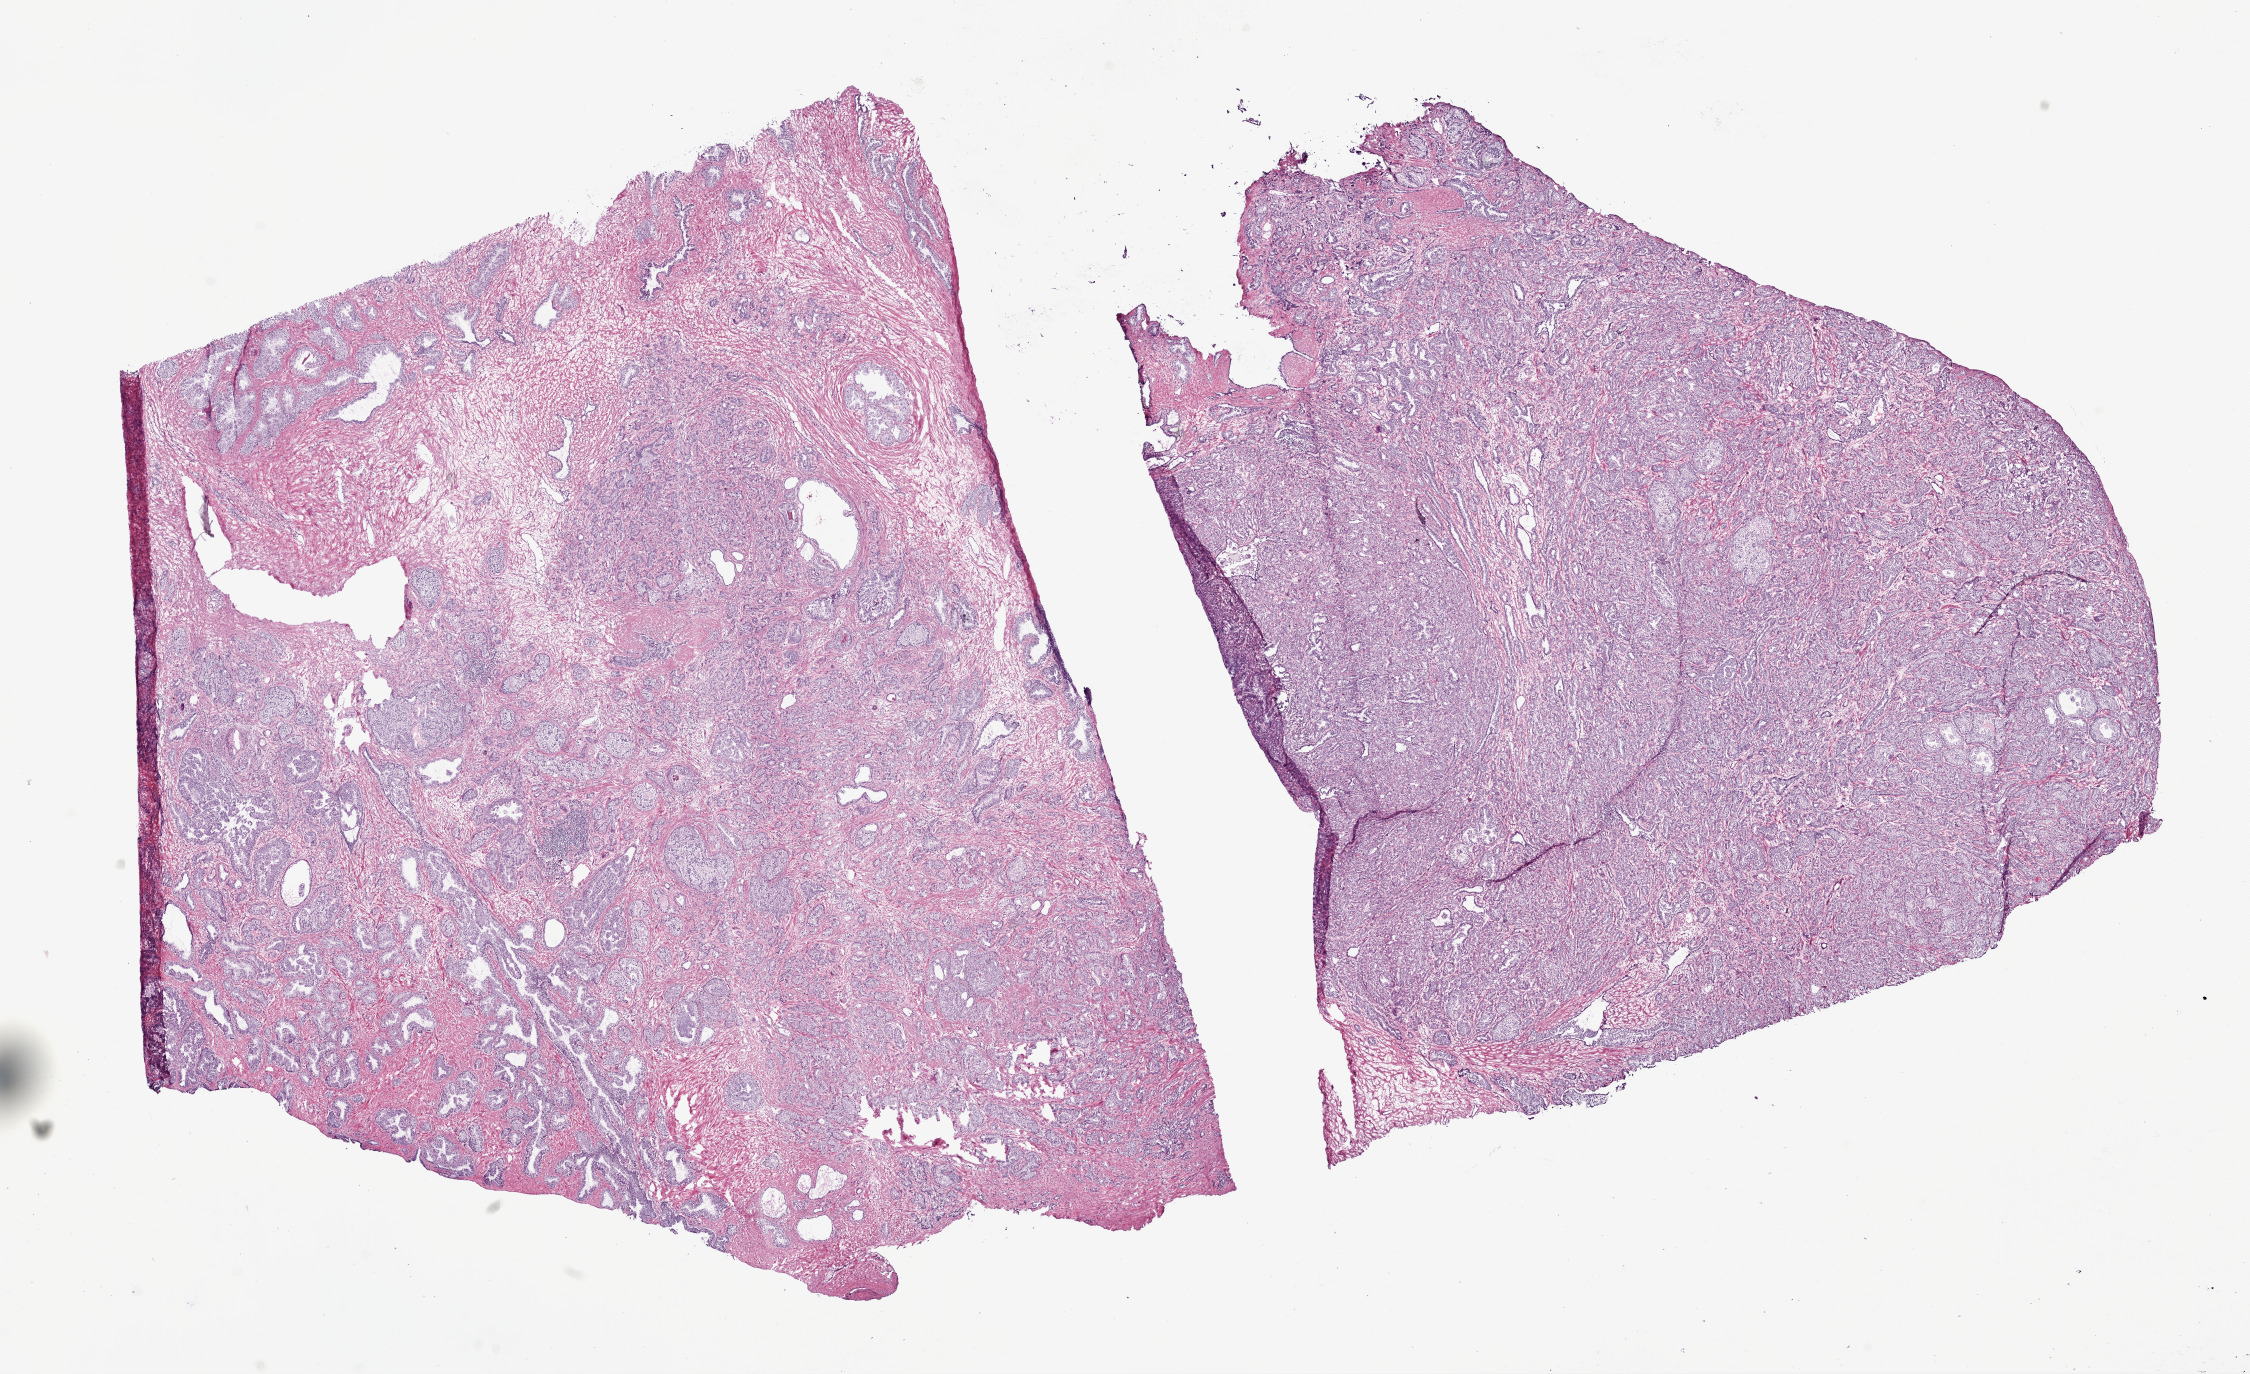
H&E-stained whole-slide image — low-resolution overview of the scanned area, about 18.1 x 11.0 mm; frozen section from the bottom of the tissue portion; primary tumour sample from the prostate. Male patient; age at initial diagnosis 60 years. Gleason score: 7 (3+4). Slide review estimates, as recorded: tumour cells 70%, tumour nuclei 80%, normal cells 15%, stromal cells 15%, necrosis 0%. Infiltration values recorded for this section: lymphocyte infiltration 2%, monocyte infiltration 0%, neutrophil infiltration 0%.
Laterality: bilateral. Lymph nodes positive (case pathology): 0 of 17 examined. Histologic diagnosis: Acinar cell carcinoma (prostate gland).